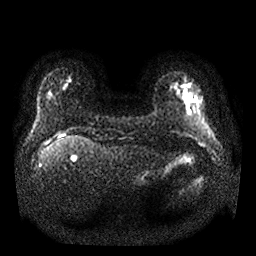
Breast MRI, one axial slice; position 3 of 25 along the scan axis; diffusion-weighted series; image 2 of 4 stored at this slice position (different b-values; order by instance number); 1.5 T; 4 mm slice thickness; 256 × 256 image matrix. Female patient.
Outlined on this slice (manually delineated by an expert):
- tumour on diffusion-weighted imaging: box from (x=182, y=92) to (x=192, y=110) px